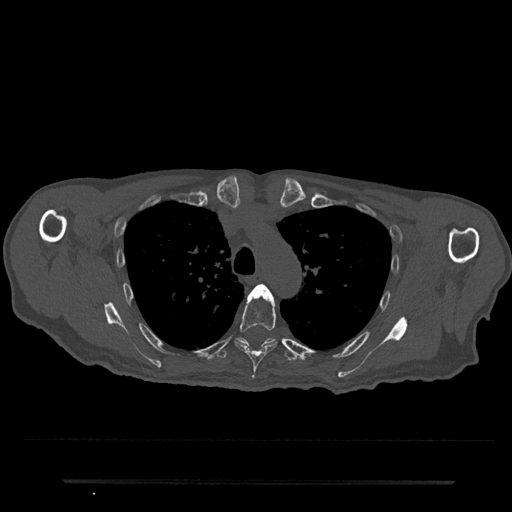
CT including the spine, one axial slice; bone window (W 1800 / L 400 HU); 0.5 mm slice thickness; 512 × 512 image matrix. Patient: male, 74 years. Case-level facts recorded for this patient, not image findings: primary cancer: prostate.
Outlined on this slice (semi-automatic segmentation, software-assisted and operator-edited):
- T4 vertebra: bounding box <255,284,266,290> (left, top, right, bottom; pixels)
- T5 vertebra: <235,287,277,379>
- T6 vertebra: <215,337,298,361>